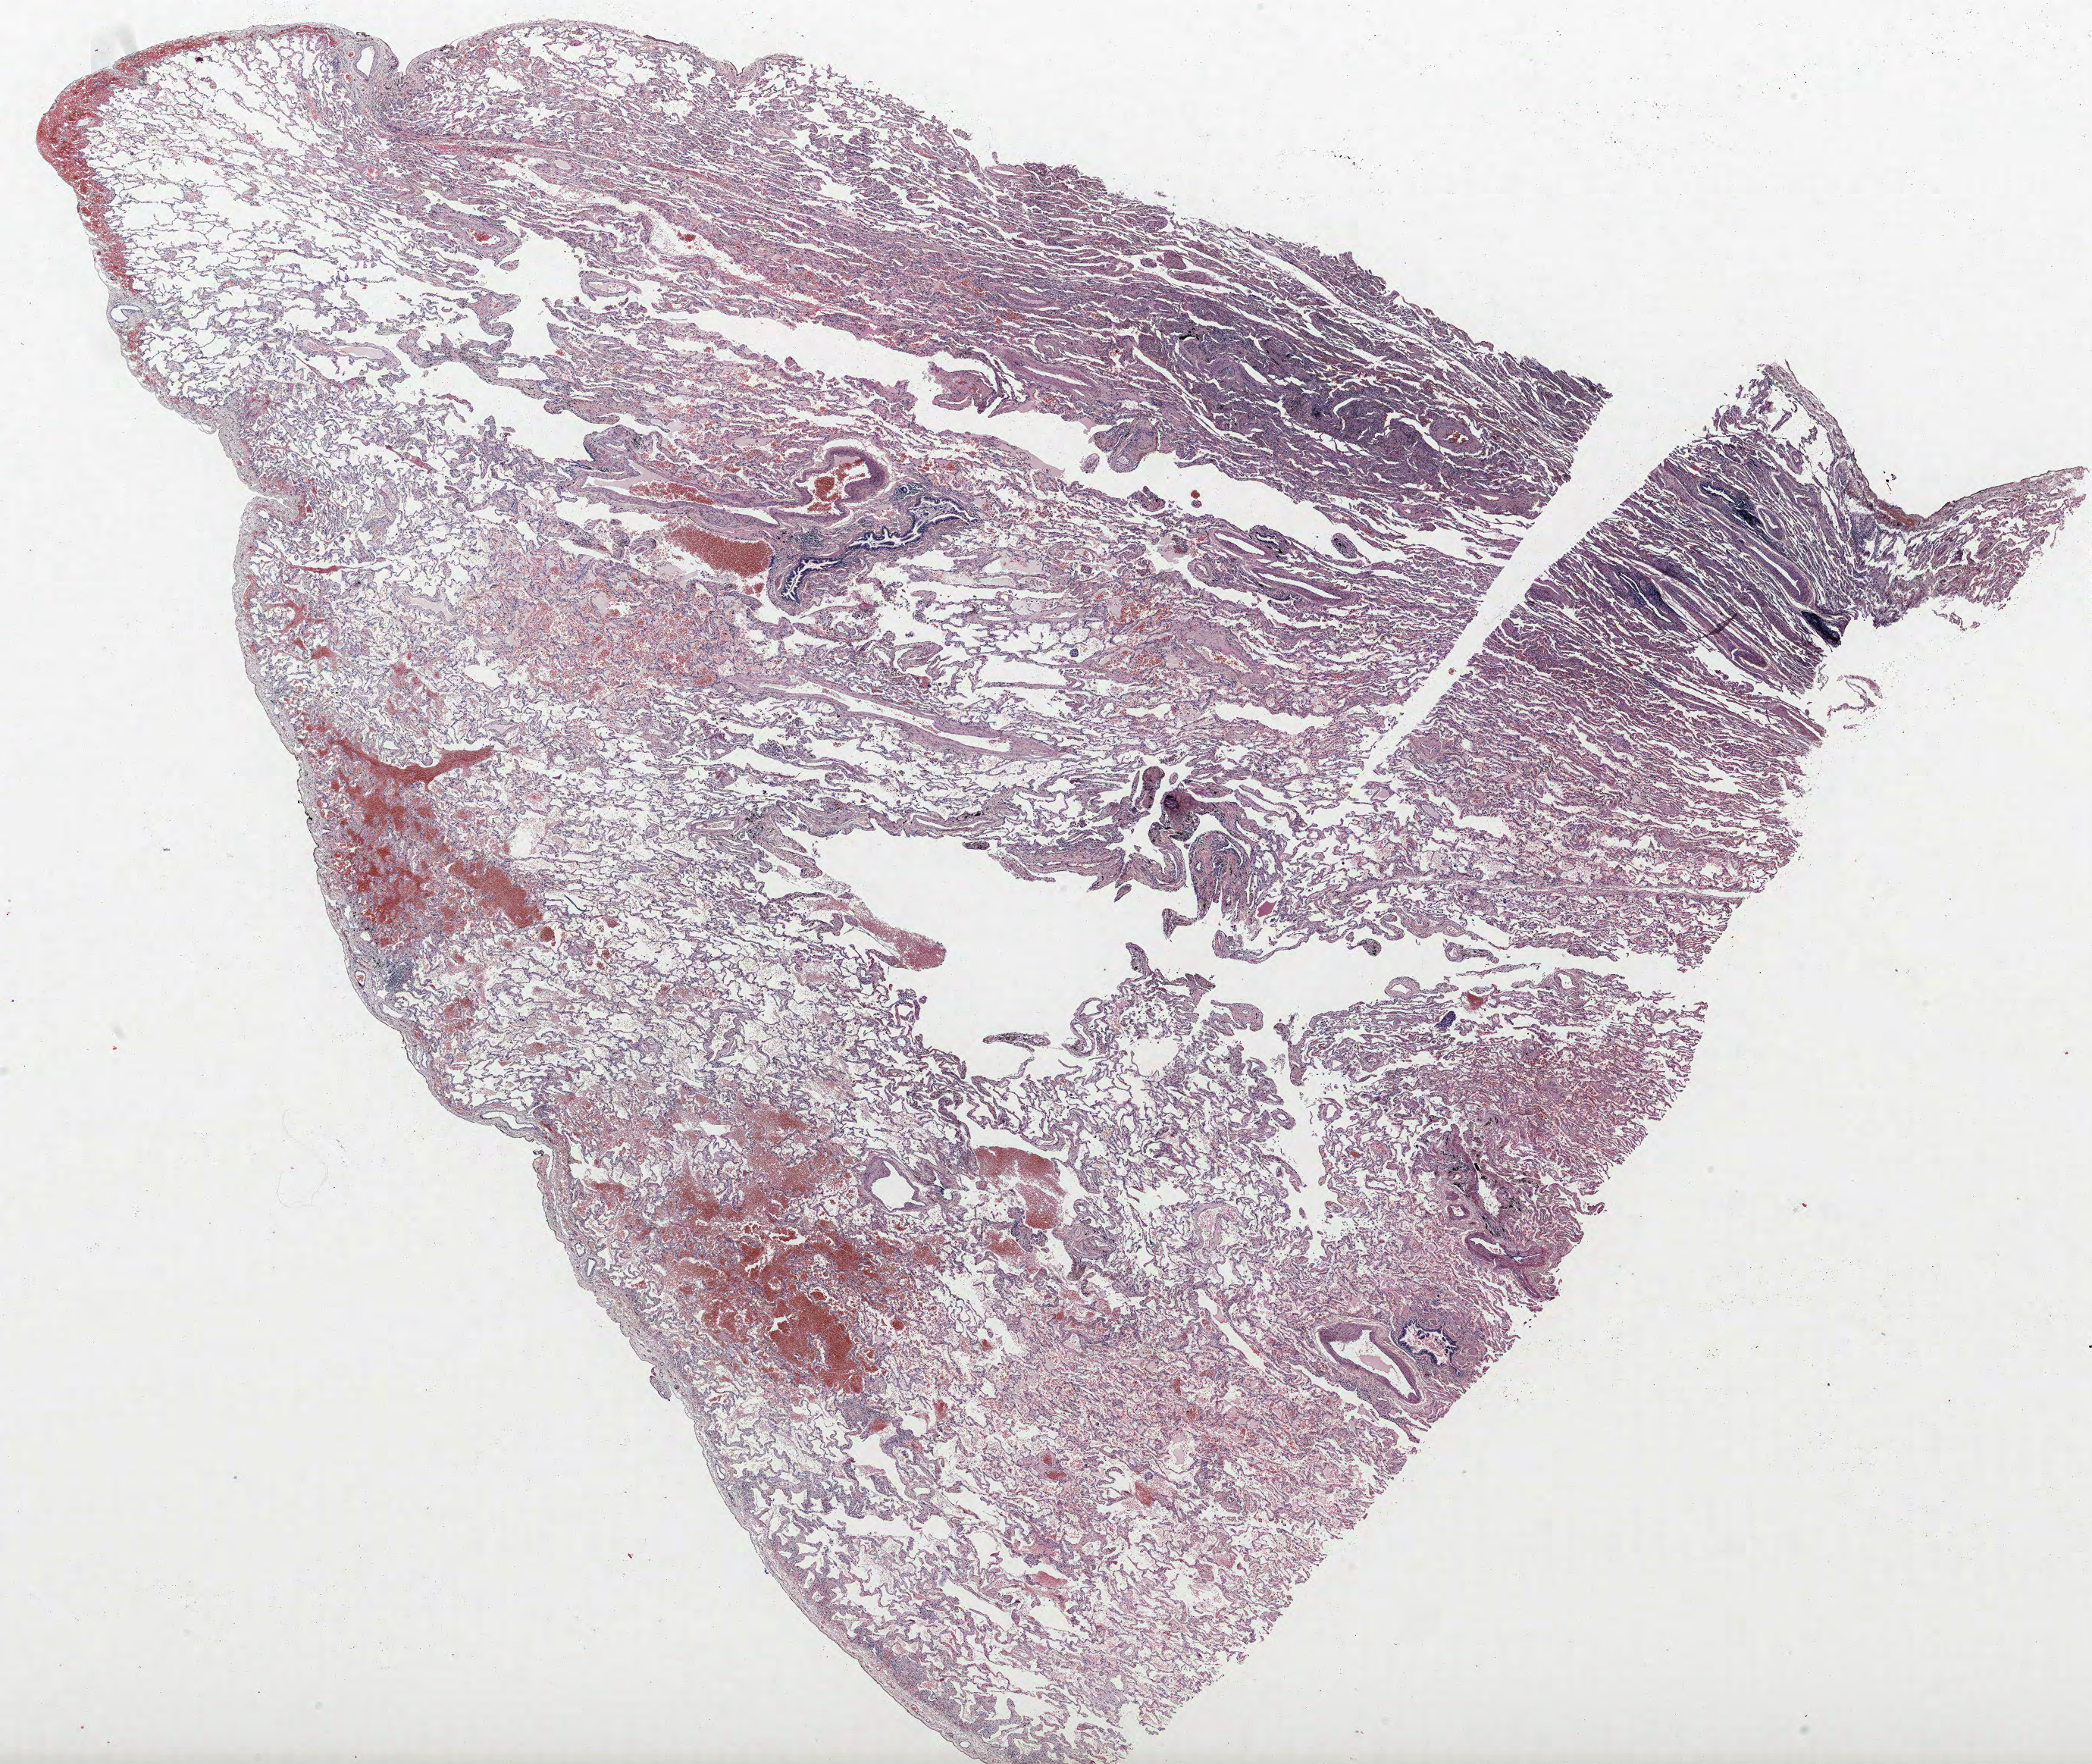
Whole-slide histology image, H&E-stained — whole scanned area (about 22.1 x 18.6 mm, slide scanned at 40x) shown as a low-resolution overview; formalin-fixed paraffin-embedded (FFPE) section; lung. Male patient, aged 64 at enrolment. Grade: moderately differentiated (G2).
* participant's lung-cancer diagnosis: Squamous cell carcinoma, NOS
* tumour size (pathology): 21 mm
* stage (AJCC 6th edition): IIB
* primary tumour location (clinical record): right upper lobe